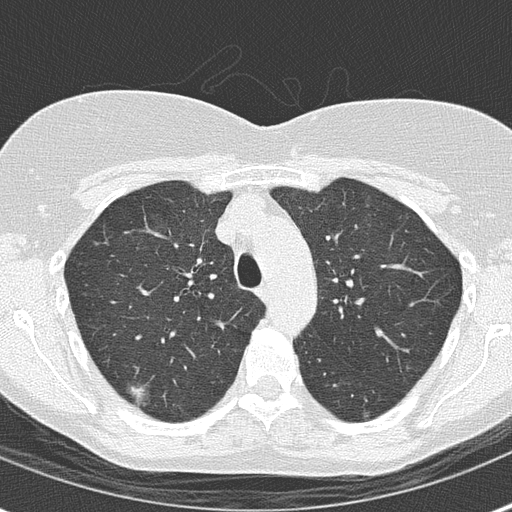
Axial slice from a low-dose chest CT screening exam. Baseline screening round. Lung window (W 1500 / L -600 HU). 2 mm slice thickness. 120 kVp. Slice 43 of 147 in the series. Female, age 56 years at enrolment.
Lesion marked by an expert reader, box from (x=111, y=364) to (x=161, y=416) px. The screening reader recorded 2 non-calcified nodules or masses ≥4 mm on this exam; which of them this box marks is not recorded. Later outcome: lung cancer diagnosed 457 days after this screen — bronchiolo-alveolar adenocarcinoma, NOS, right upper lobe, well differentiated (G1), stage IA (AJCC 6th edition), 15 mm at pathology.